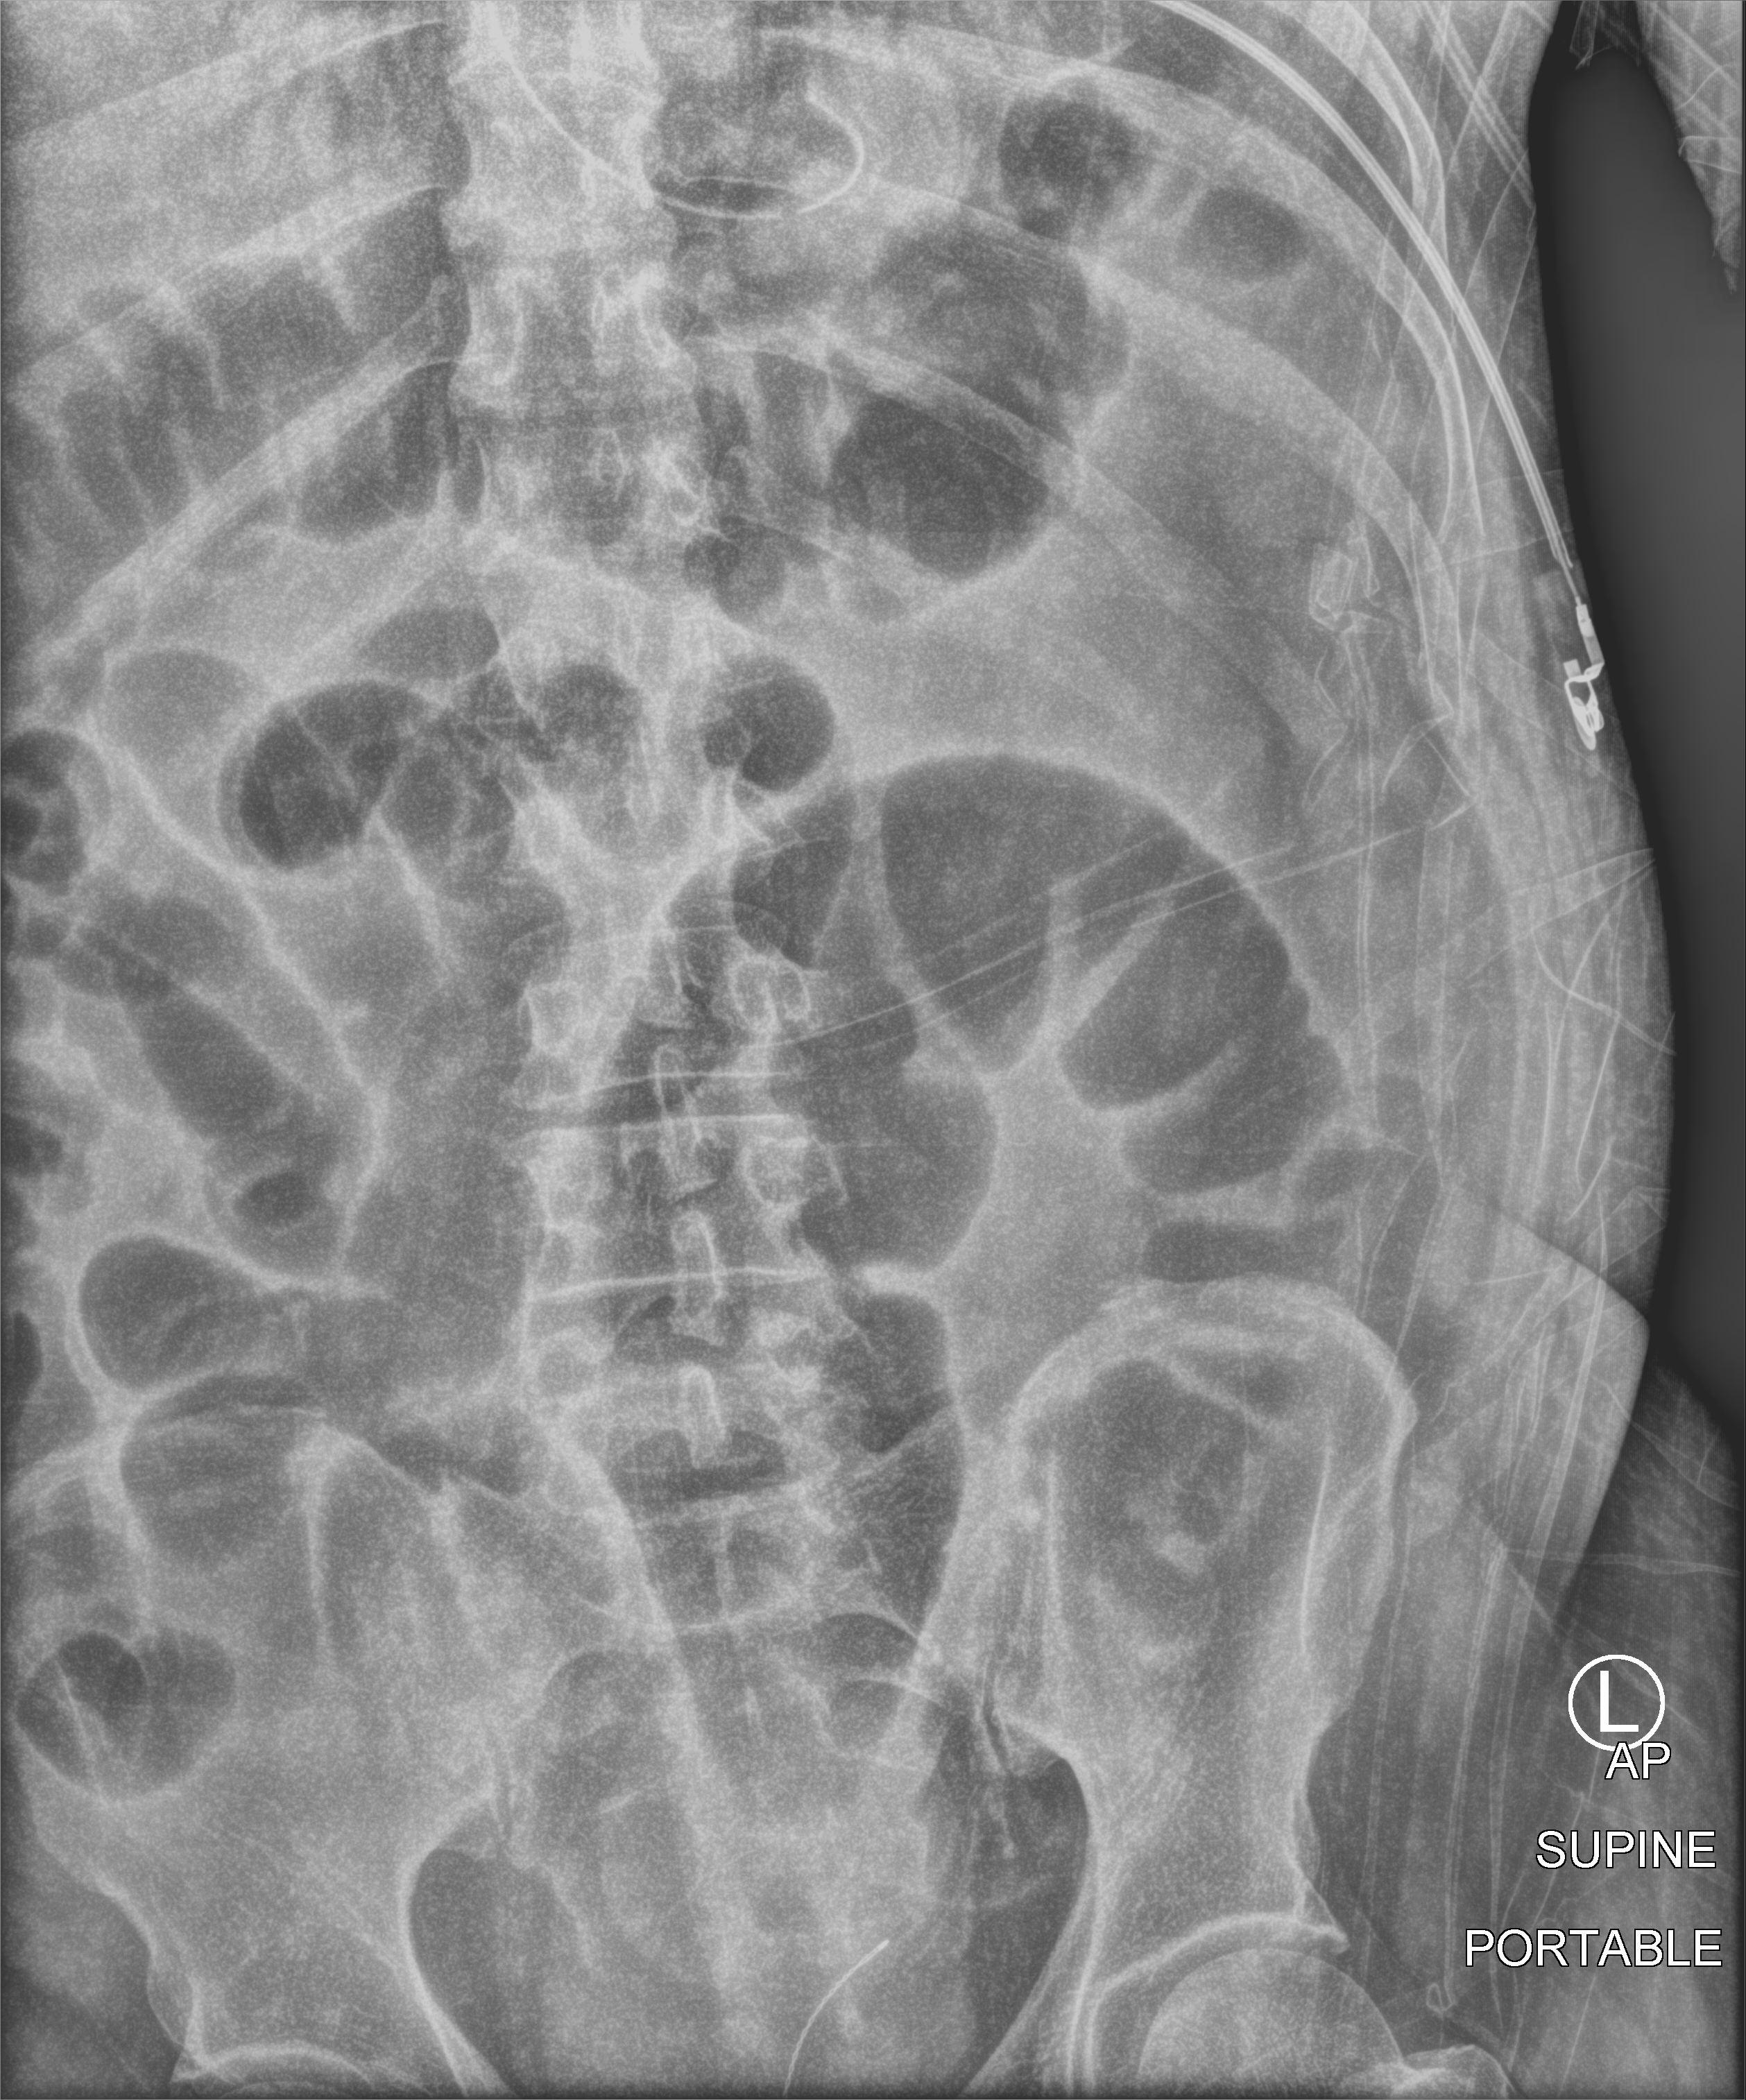
Abdomen X-ray (portable). Male patient hospitalised with COVID-19, age 18–59 years.
Hospital-stay facts (about this admission, not read from this image; timing relative to this image not recorded):
- mechanically ventilated during this hospital stay: yes
- admitted to intensive care during this hospital stay: yes